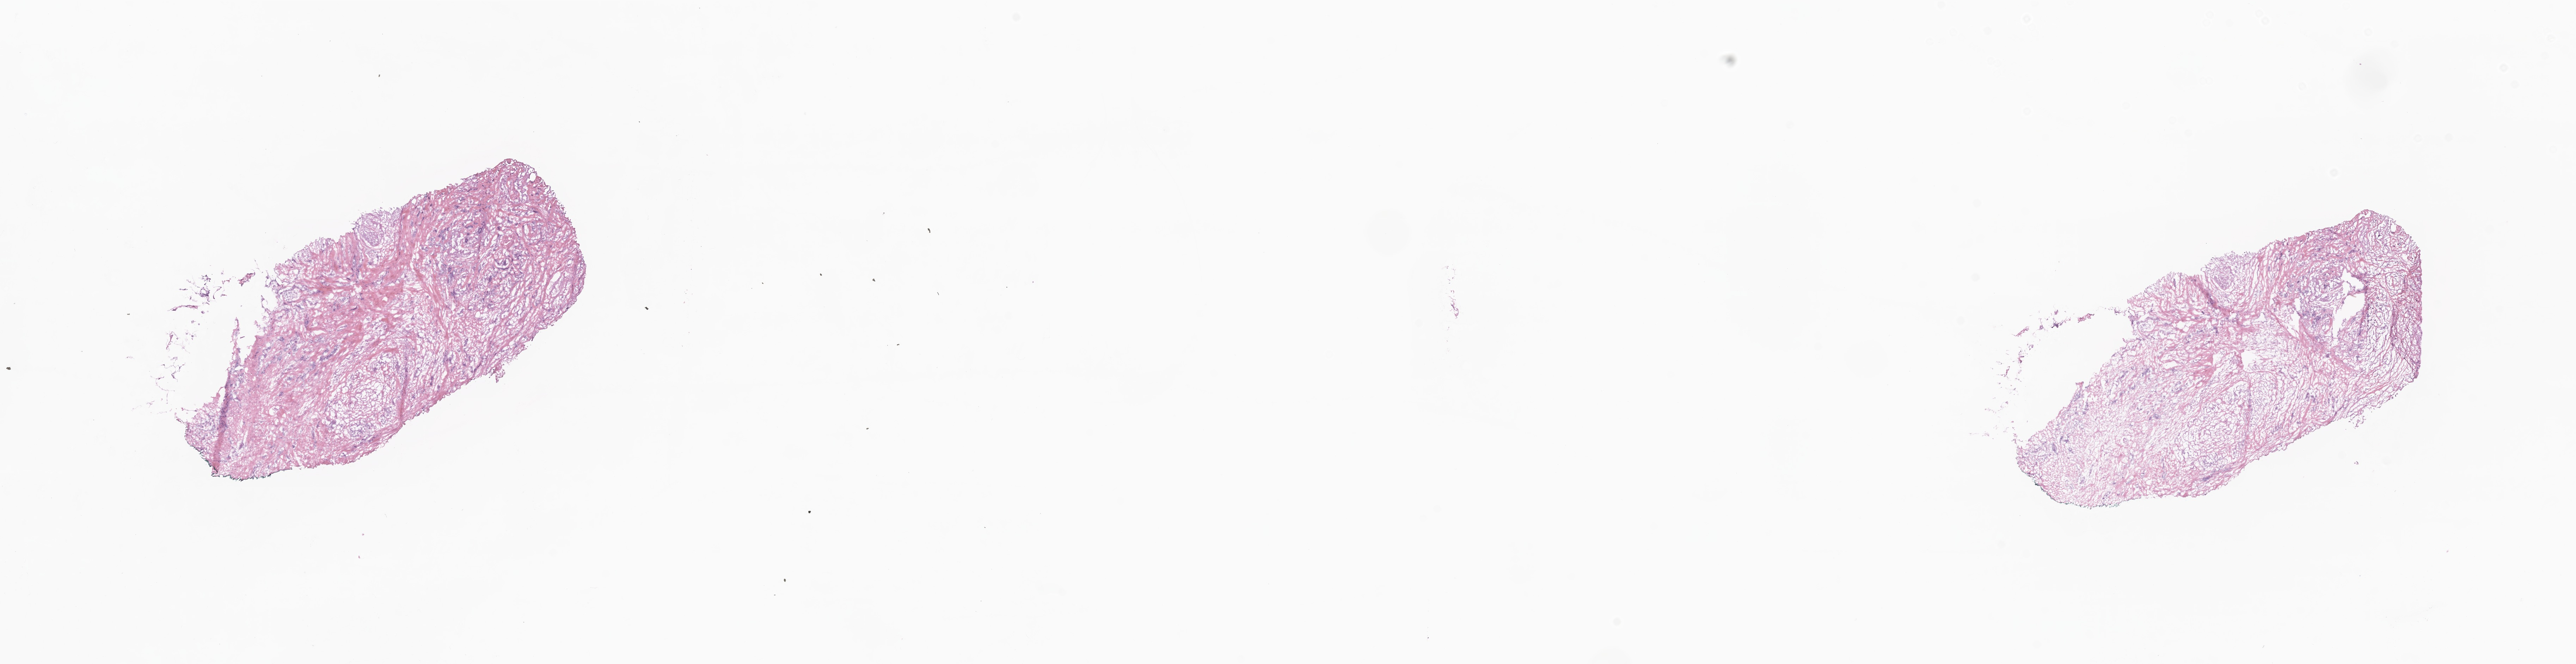
Digitized haematoxylin and eosin-stained section — whole scanned area (about 30.8 x 7.9 mm) shown as a low-resolution overview, cryosection, primary tumor, site: breast. Female patient; age at initial diagnosis 67 years.
Diagnosis: Infiltrating duct carcinoma, NOS.